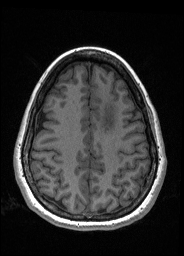
Pre-operative brain MRI before brain-tumour surgery, one axial slice. Position 60 of 176 along the scan axis. T1-weighted post-contrast. 1 mm slice thickness. 184 × 256 image matrix, field of view 180 × 250 mm. Case-level facts recorded for this patient, not image findings: histopathology: Oligodendroglioma; WHO grade: 2; IDH mutation: yes; tumour location: Left Frontal.
Outlined on this slice (manually delineated by an expert):
- tumour: bounding box [x1, y1, x2, y2] px = [100, 97, 117, 133]